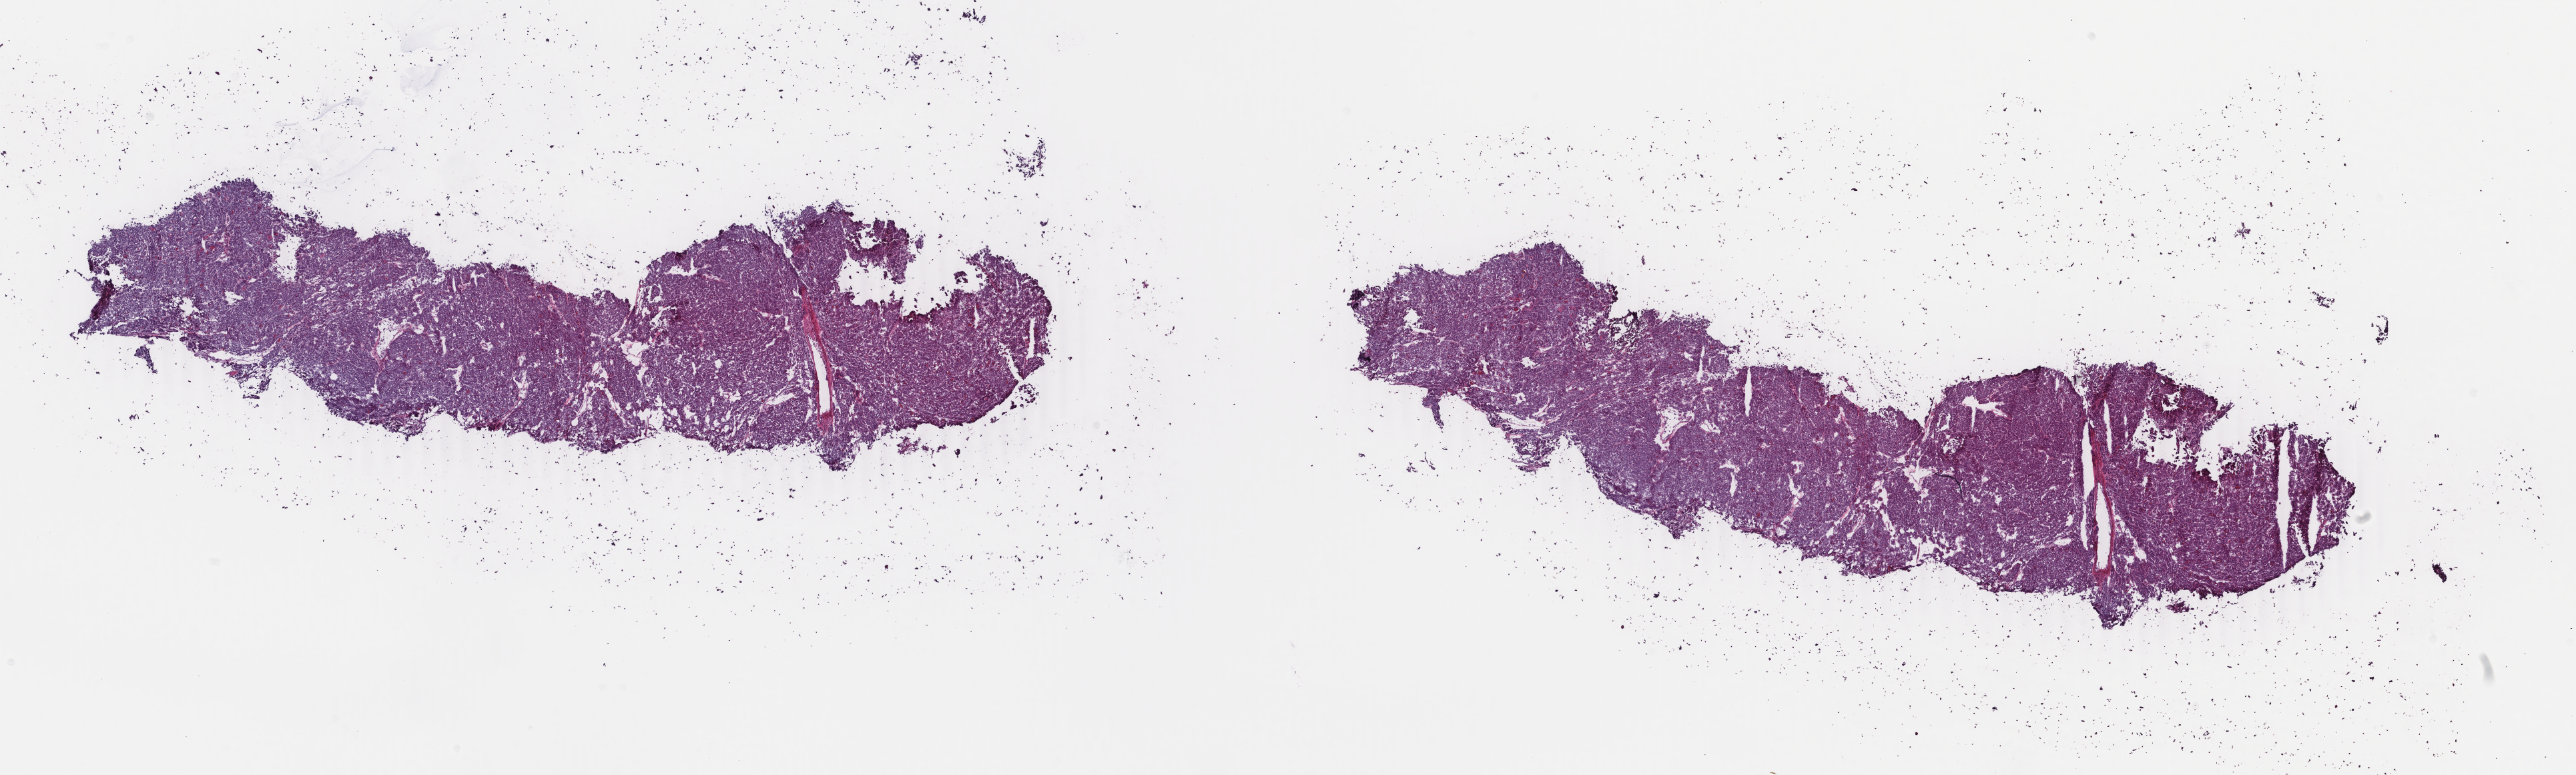
Digitized H&E tissue section (whole slide), low-resolution overview of the scanned area, about 30.7 x 9.2 mm (from a 40x scan). Frozen section from the bottom of the tissue portion. Sample: primary tumour, thyroid. Female patient; age at initial diagnosis 19 years. Composition of this section per pathologist review: tumour cells 100%, tumour nuclei 98%, normal cells 0%, stromal cells 0%, necrosis 0%. Inflammatory infiltration, as recorded: lymphocyte infiltration 0%, monocyte infiltration 0%, neutrophil infiltration 0%.
• histologic diagnosis: Papillary carcinoma, follicular variant (thyroid gland)
• AJCC pathologic stage: I (7th edition)